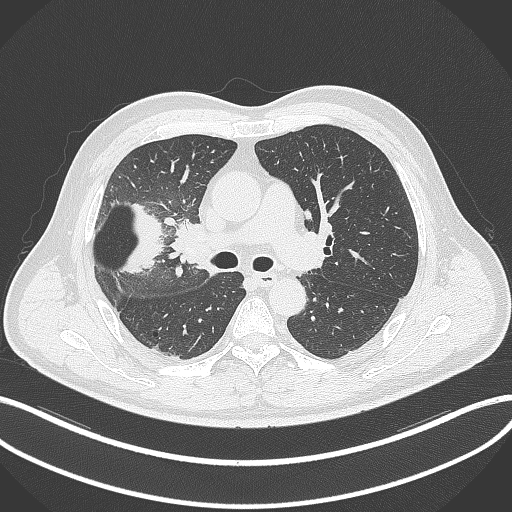
Chest CT, one axial slice. Slice 203 of 348 in the series (ordered by position). Reconstruction kernel B70f. 120 kVp. Lung window (W 1500 / L -600 HU). 1 mm slice thickness. 512 × 512 image matrix. Male patient, age 55 years. Case-level facts recorded for this patient, not image findings: clinical TNM (as recorded): T3 N2 M1.
Annotated regions visible in this slice (rectangle marked by the reading radiologist):
- lung tumour (recorded histology: adenocarcinoma): box from (x=119, y=200) to (x=169, y=277) px